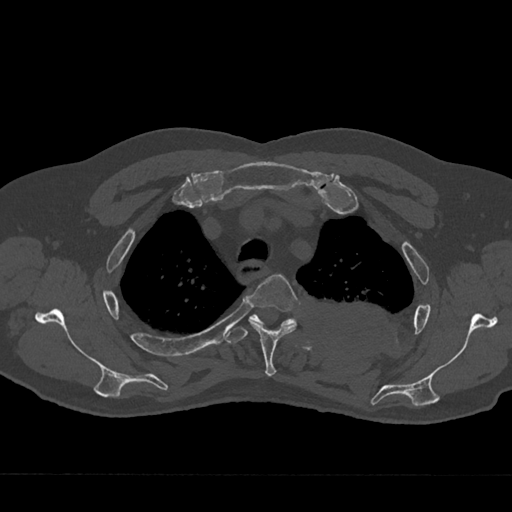
CT including the spine, one axial slice. Position 552 of 797 along the scan axis. Reconstruction kernel Br40s/3. 120 kVp. Bone window (W 1800 / L 400 HU). 512 × 512 image matrix, field of view 377 × 377 mm. Patient: male, 75 years. Case-level facts recorded for this patient, not image findings: primary cancer: renal.
Outlined on this slice (semi-automatically segmented with operator editing):
- T3 vertebra: bounding box [x1, y1, x2, y2] px = [248, 274, 299, 376]
- T4 vertebra: [226, 314, 297, 344]